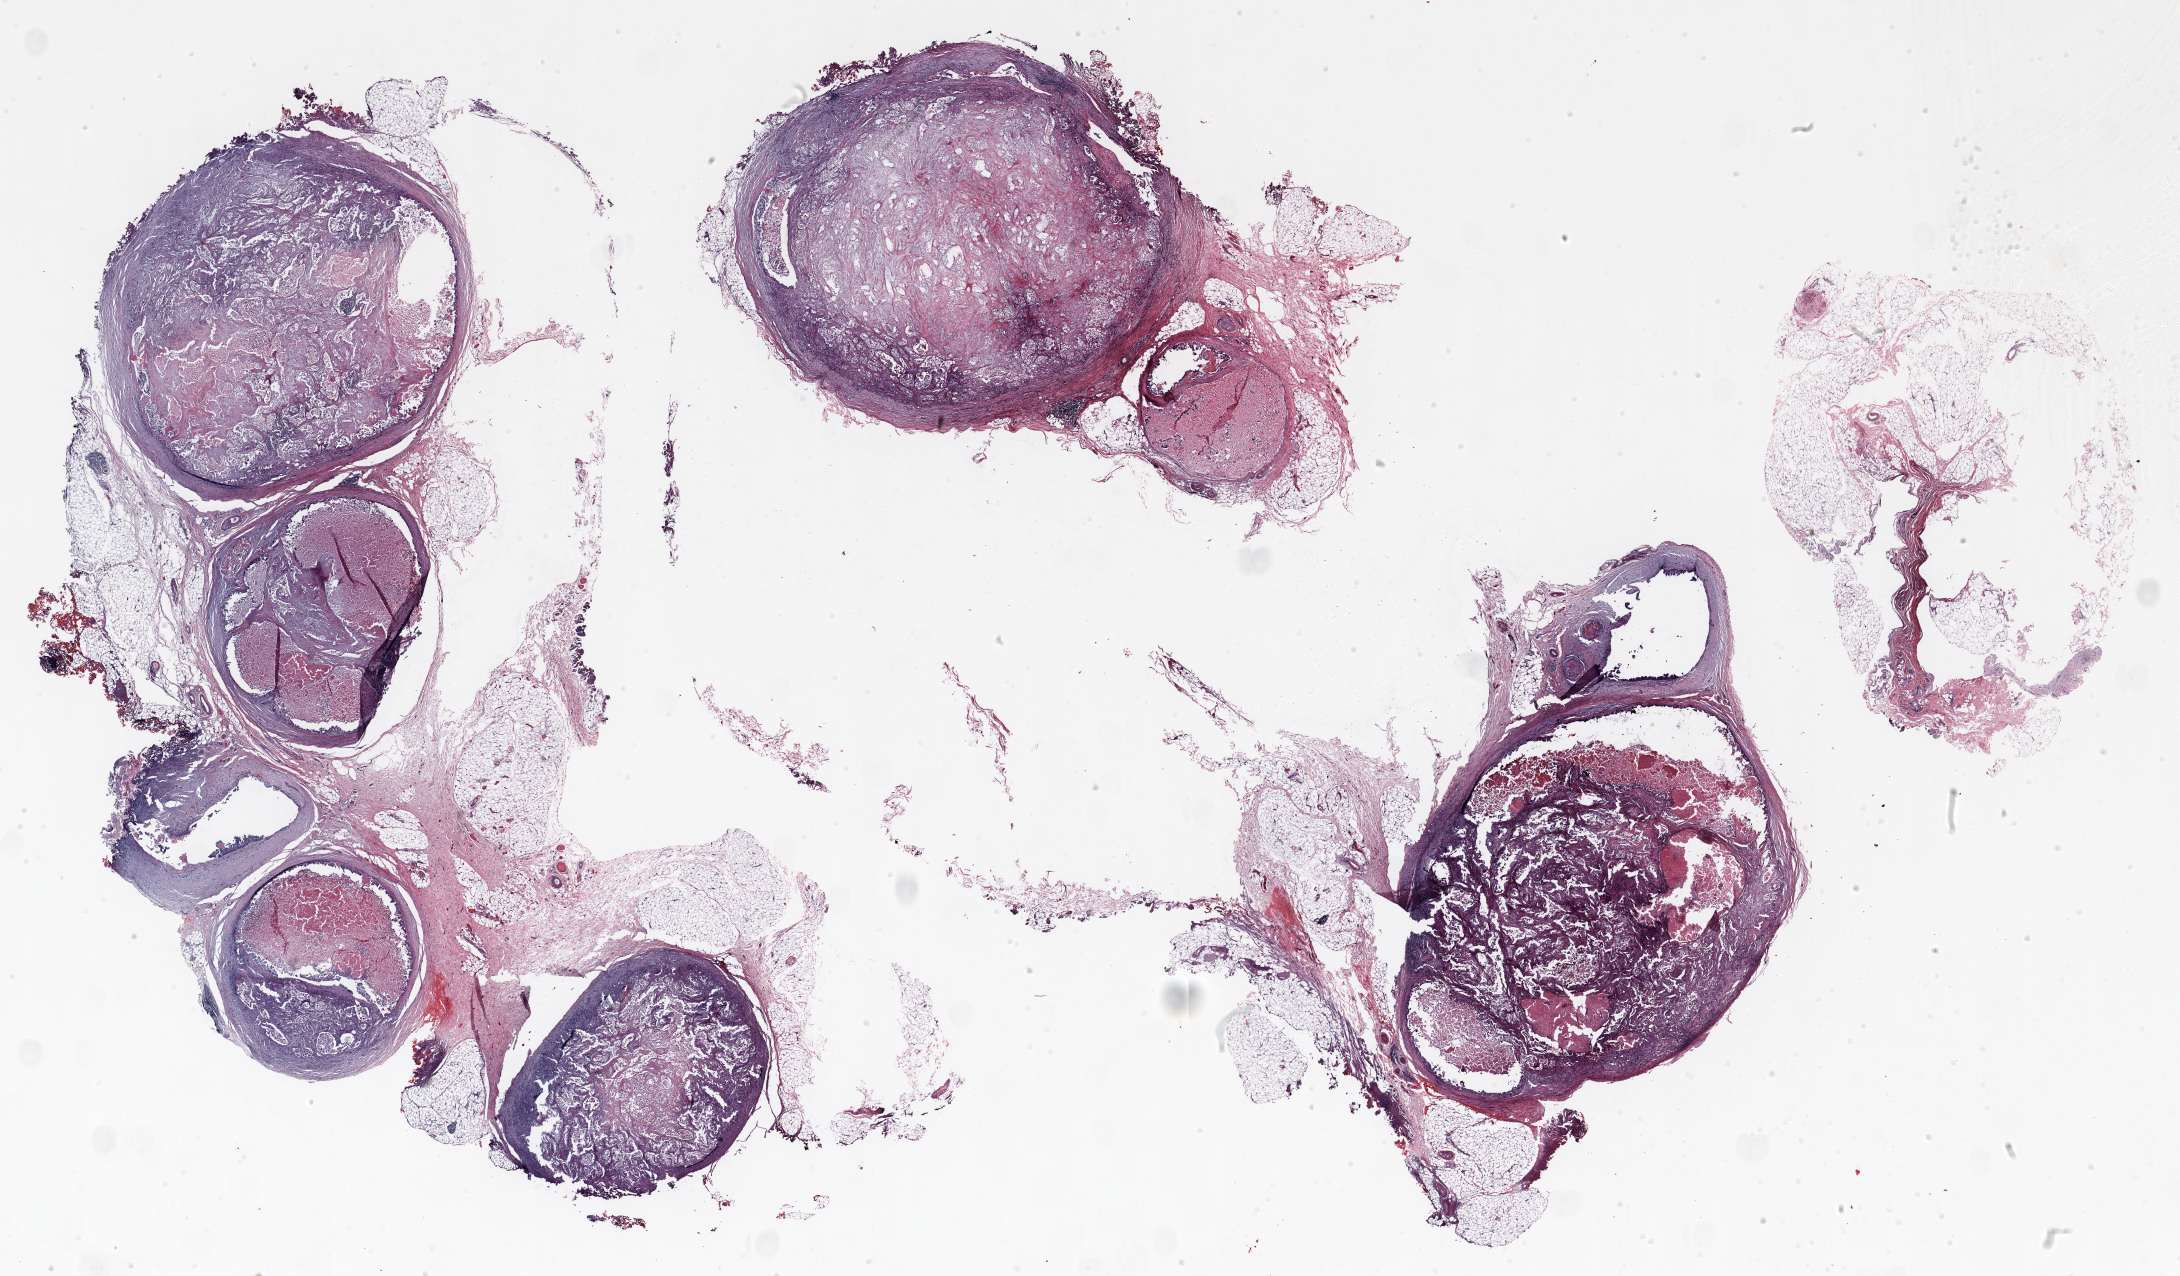
Whole-slide histology image, H&E, whole scanned area (about 35.0 x 20.5 mm, from a 20x scan) shown as a low-resolution overview. FFPE section. Lung tissue. Male patient, aged 58 at enrolment. Grade: cannot be assessed (GX).
* tumour size (pathology): 24 mm
* participant's lung-cancer diagnosis: Adenocarcinoma, NOS
* stage (AJCC 6th edition): IV
* primary tumour location (clinical record): left upper lobe